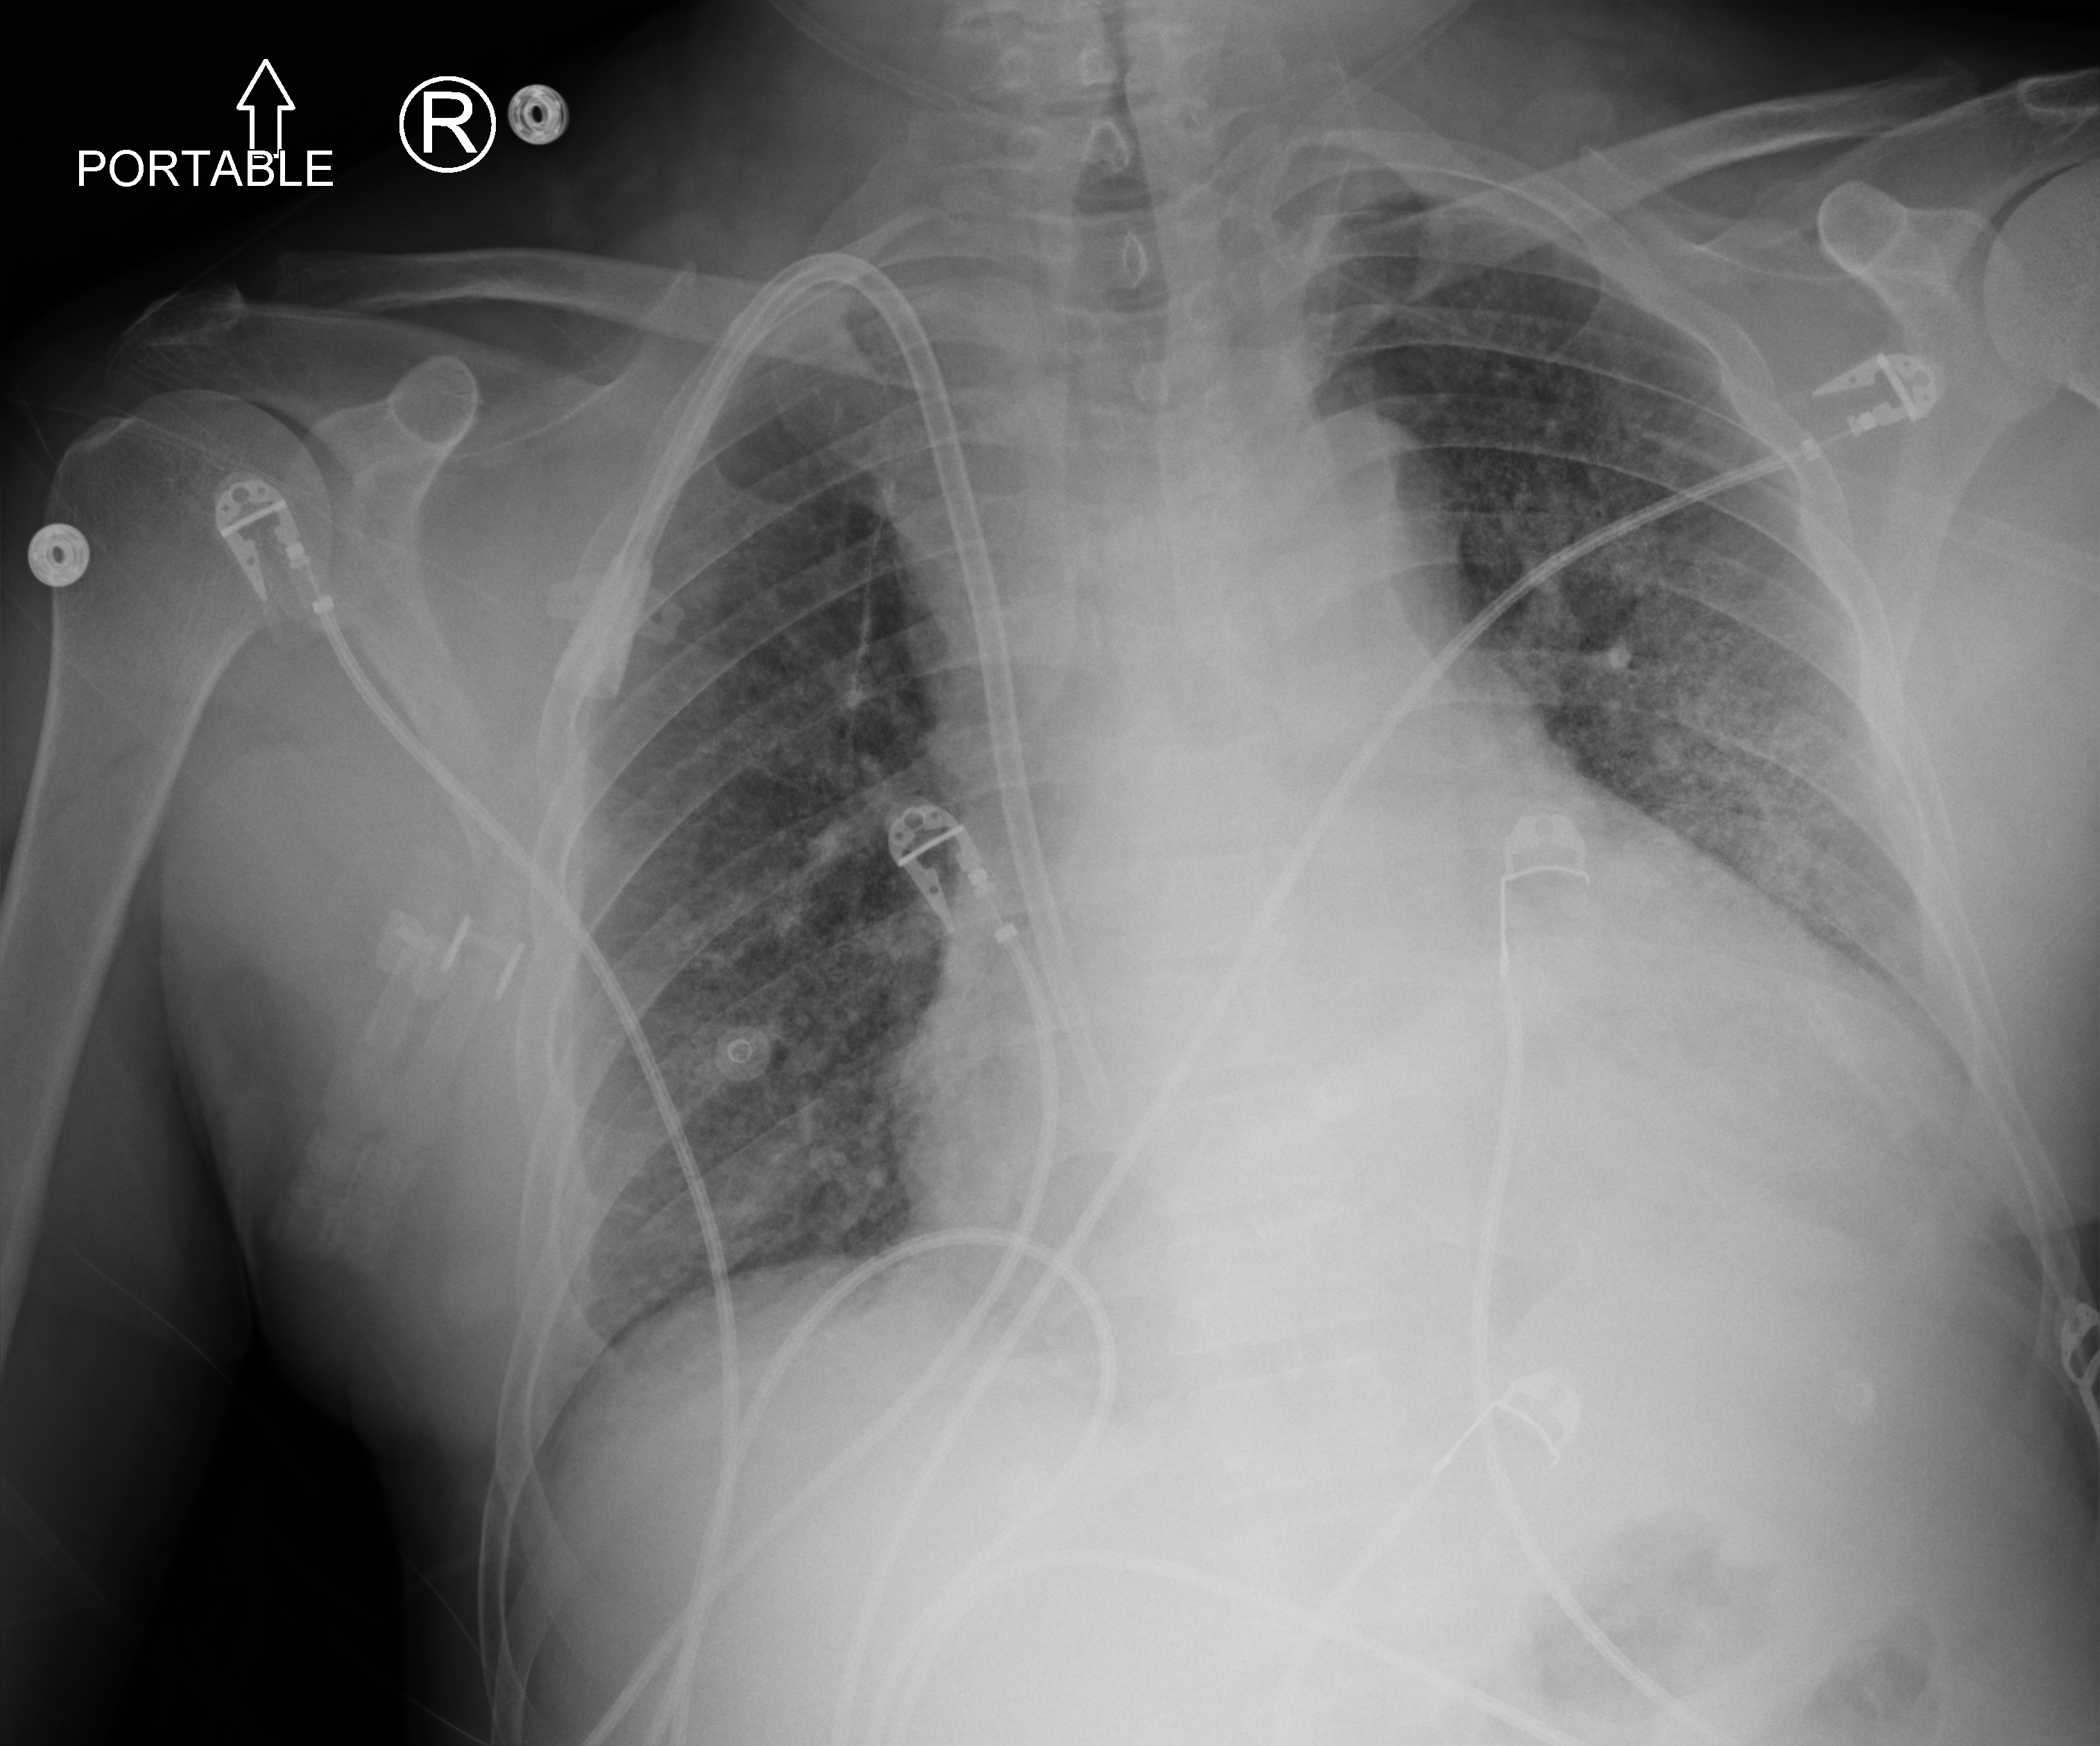
Portable chest radiograph, anteroposterior (AP) projection. Male patient hospitalised with COVID-19, age 18–59 years.
Hospital-stay facts (about this admission, not read from this image; timing relative to this image not recorded):
- admitted to intensive care during this hospital stay: no